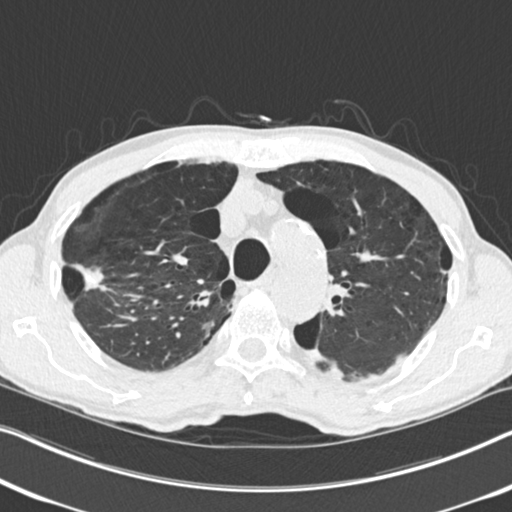
Low-dose screening chest CT, one axial slice. Slice 186 of 251 in the series (ordered by position). 120 kVp. Lung window (W 1500 / L -600 HU). 512 × 512 image matrix, field of view 334 × 334 mm.
Outlined on this slice (expert manual segmentation):
- lesion 1 (tumor, upper lobe of right lung): bounding box [x1, y1, x2, y2] px = [74, 264, 107, 291]